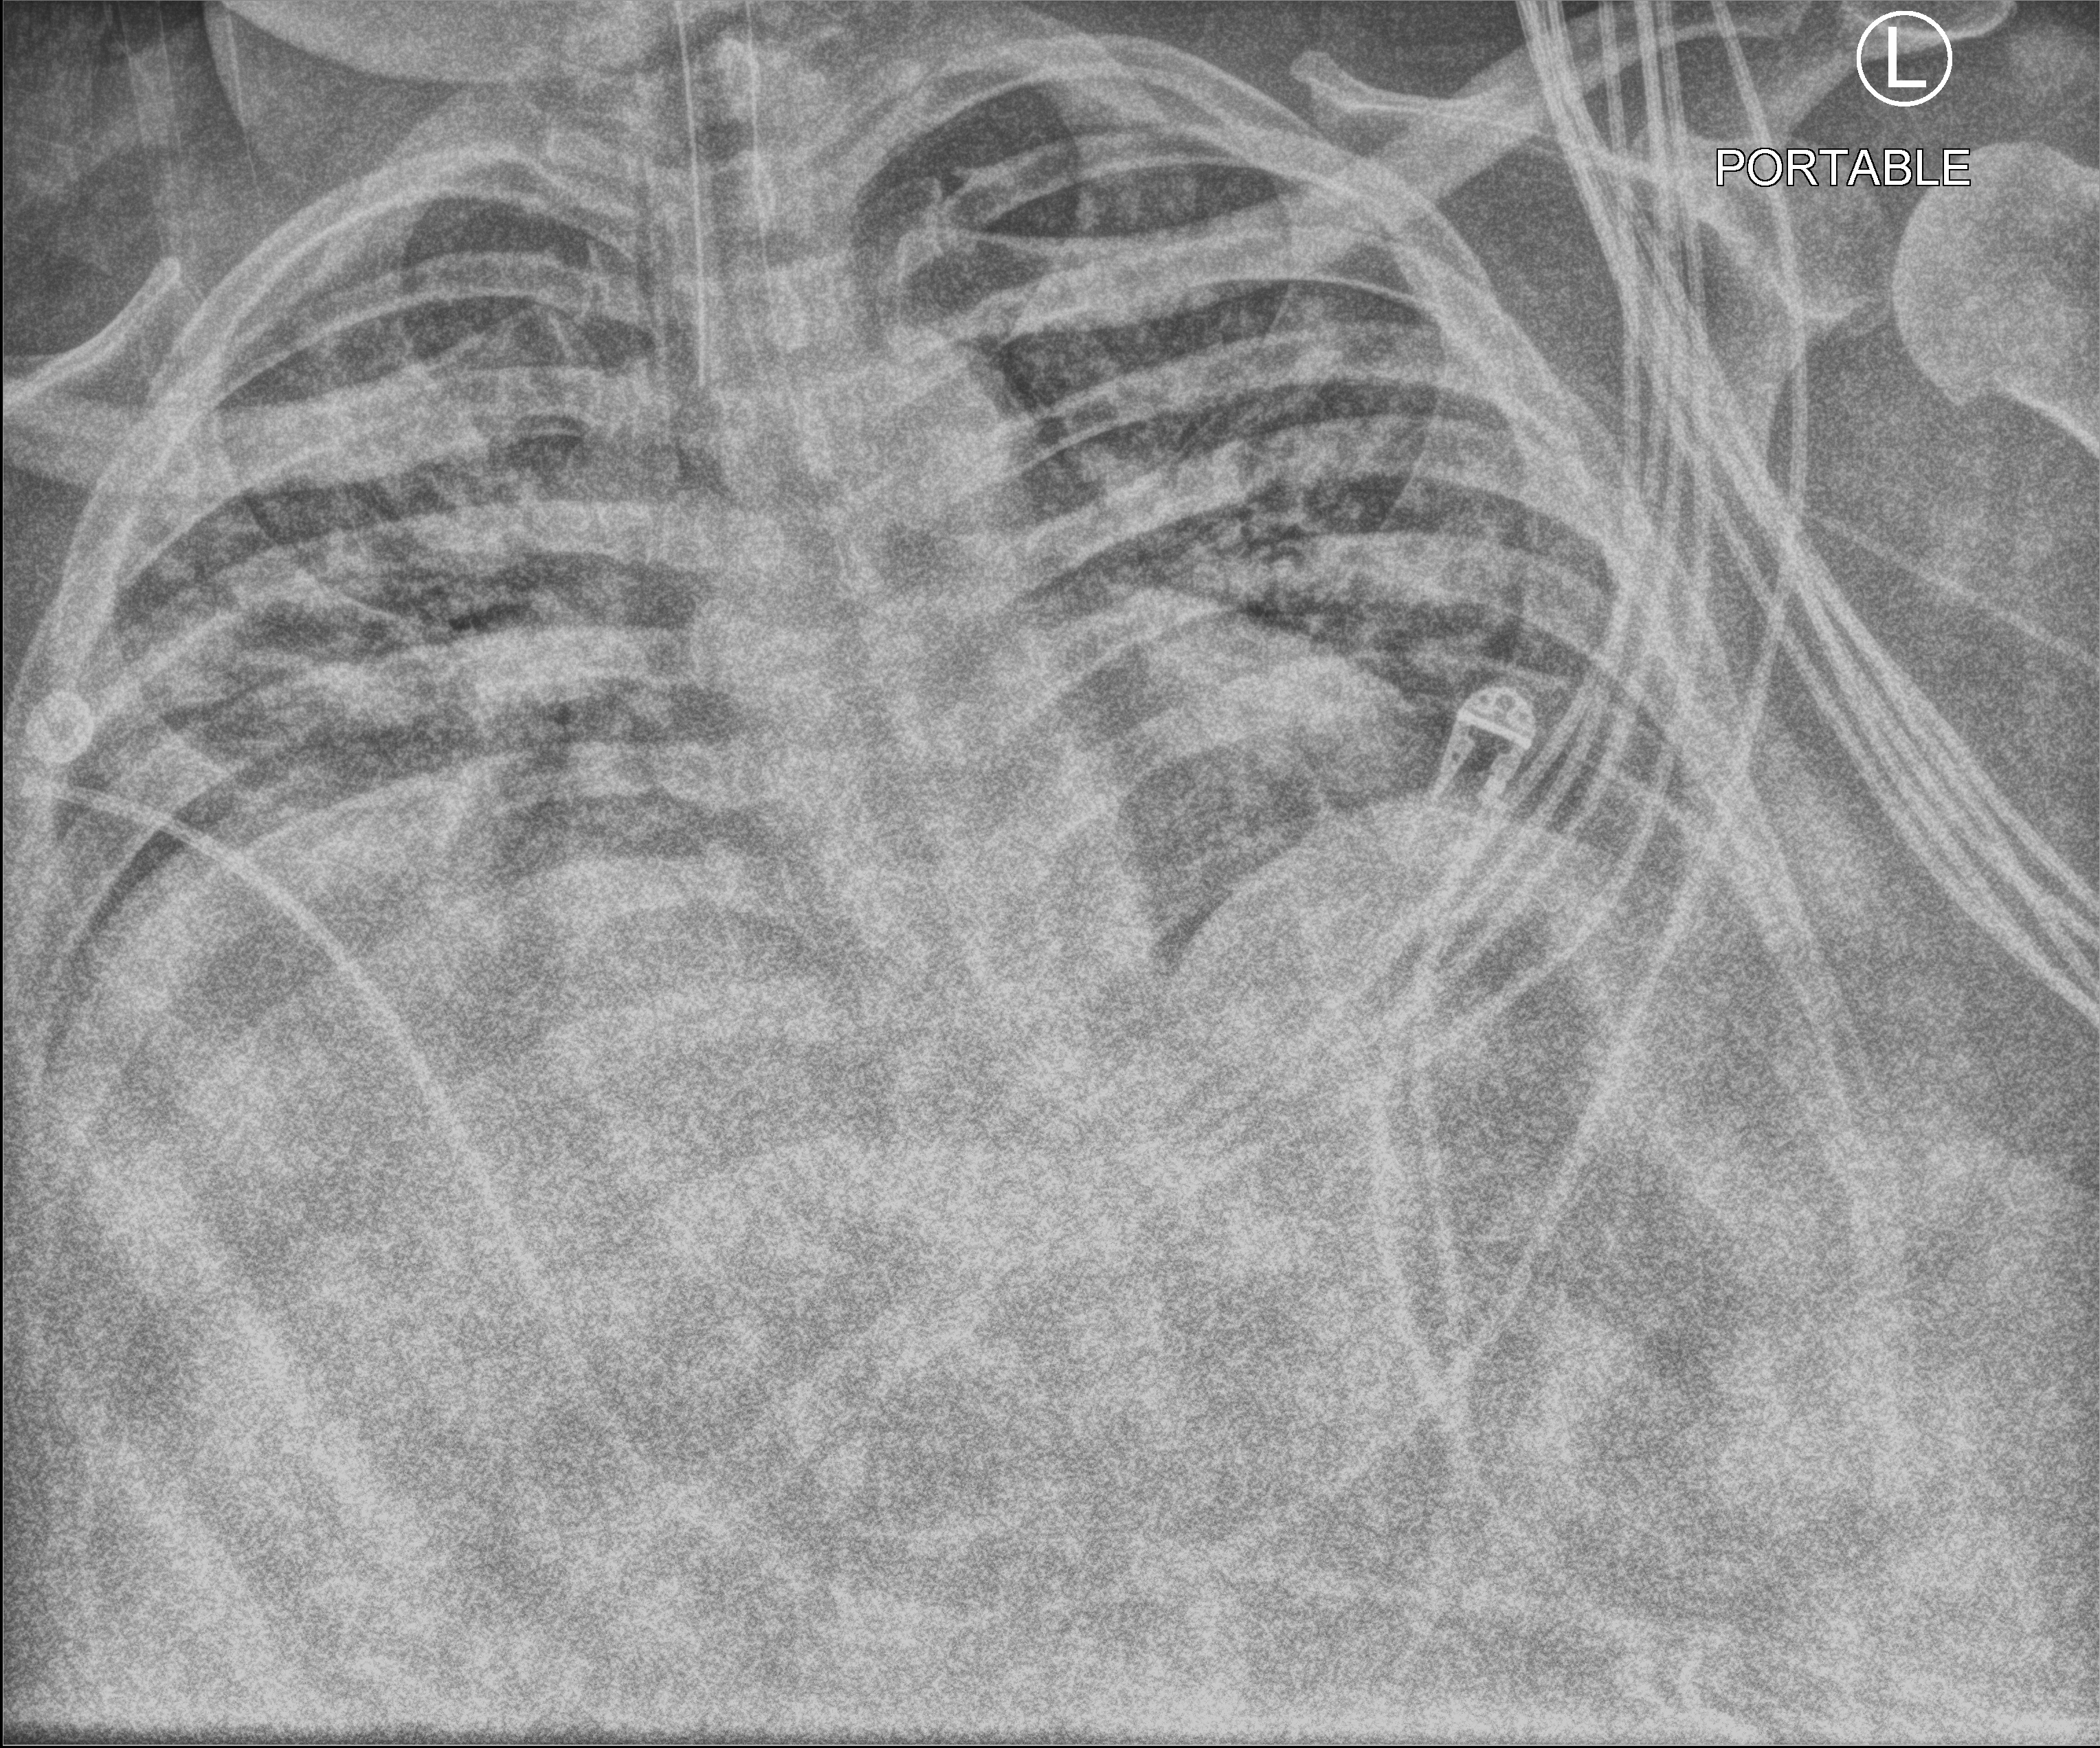
Portable chest radiograph; anteroposterior (AP) projection. Male patient hospitalised with COVID-19, age 18–59 years.
From the hospital-stay record, not from the radiograph (when in the stay this image was taken is not recorded):
- length of hospital stay: 69 days